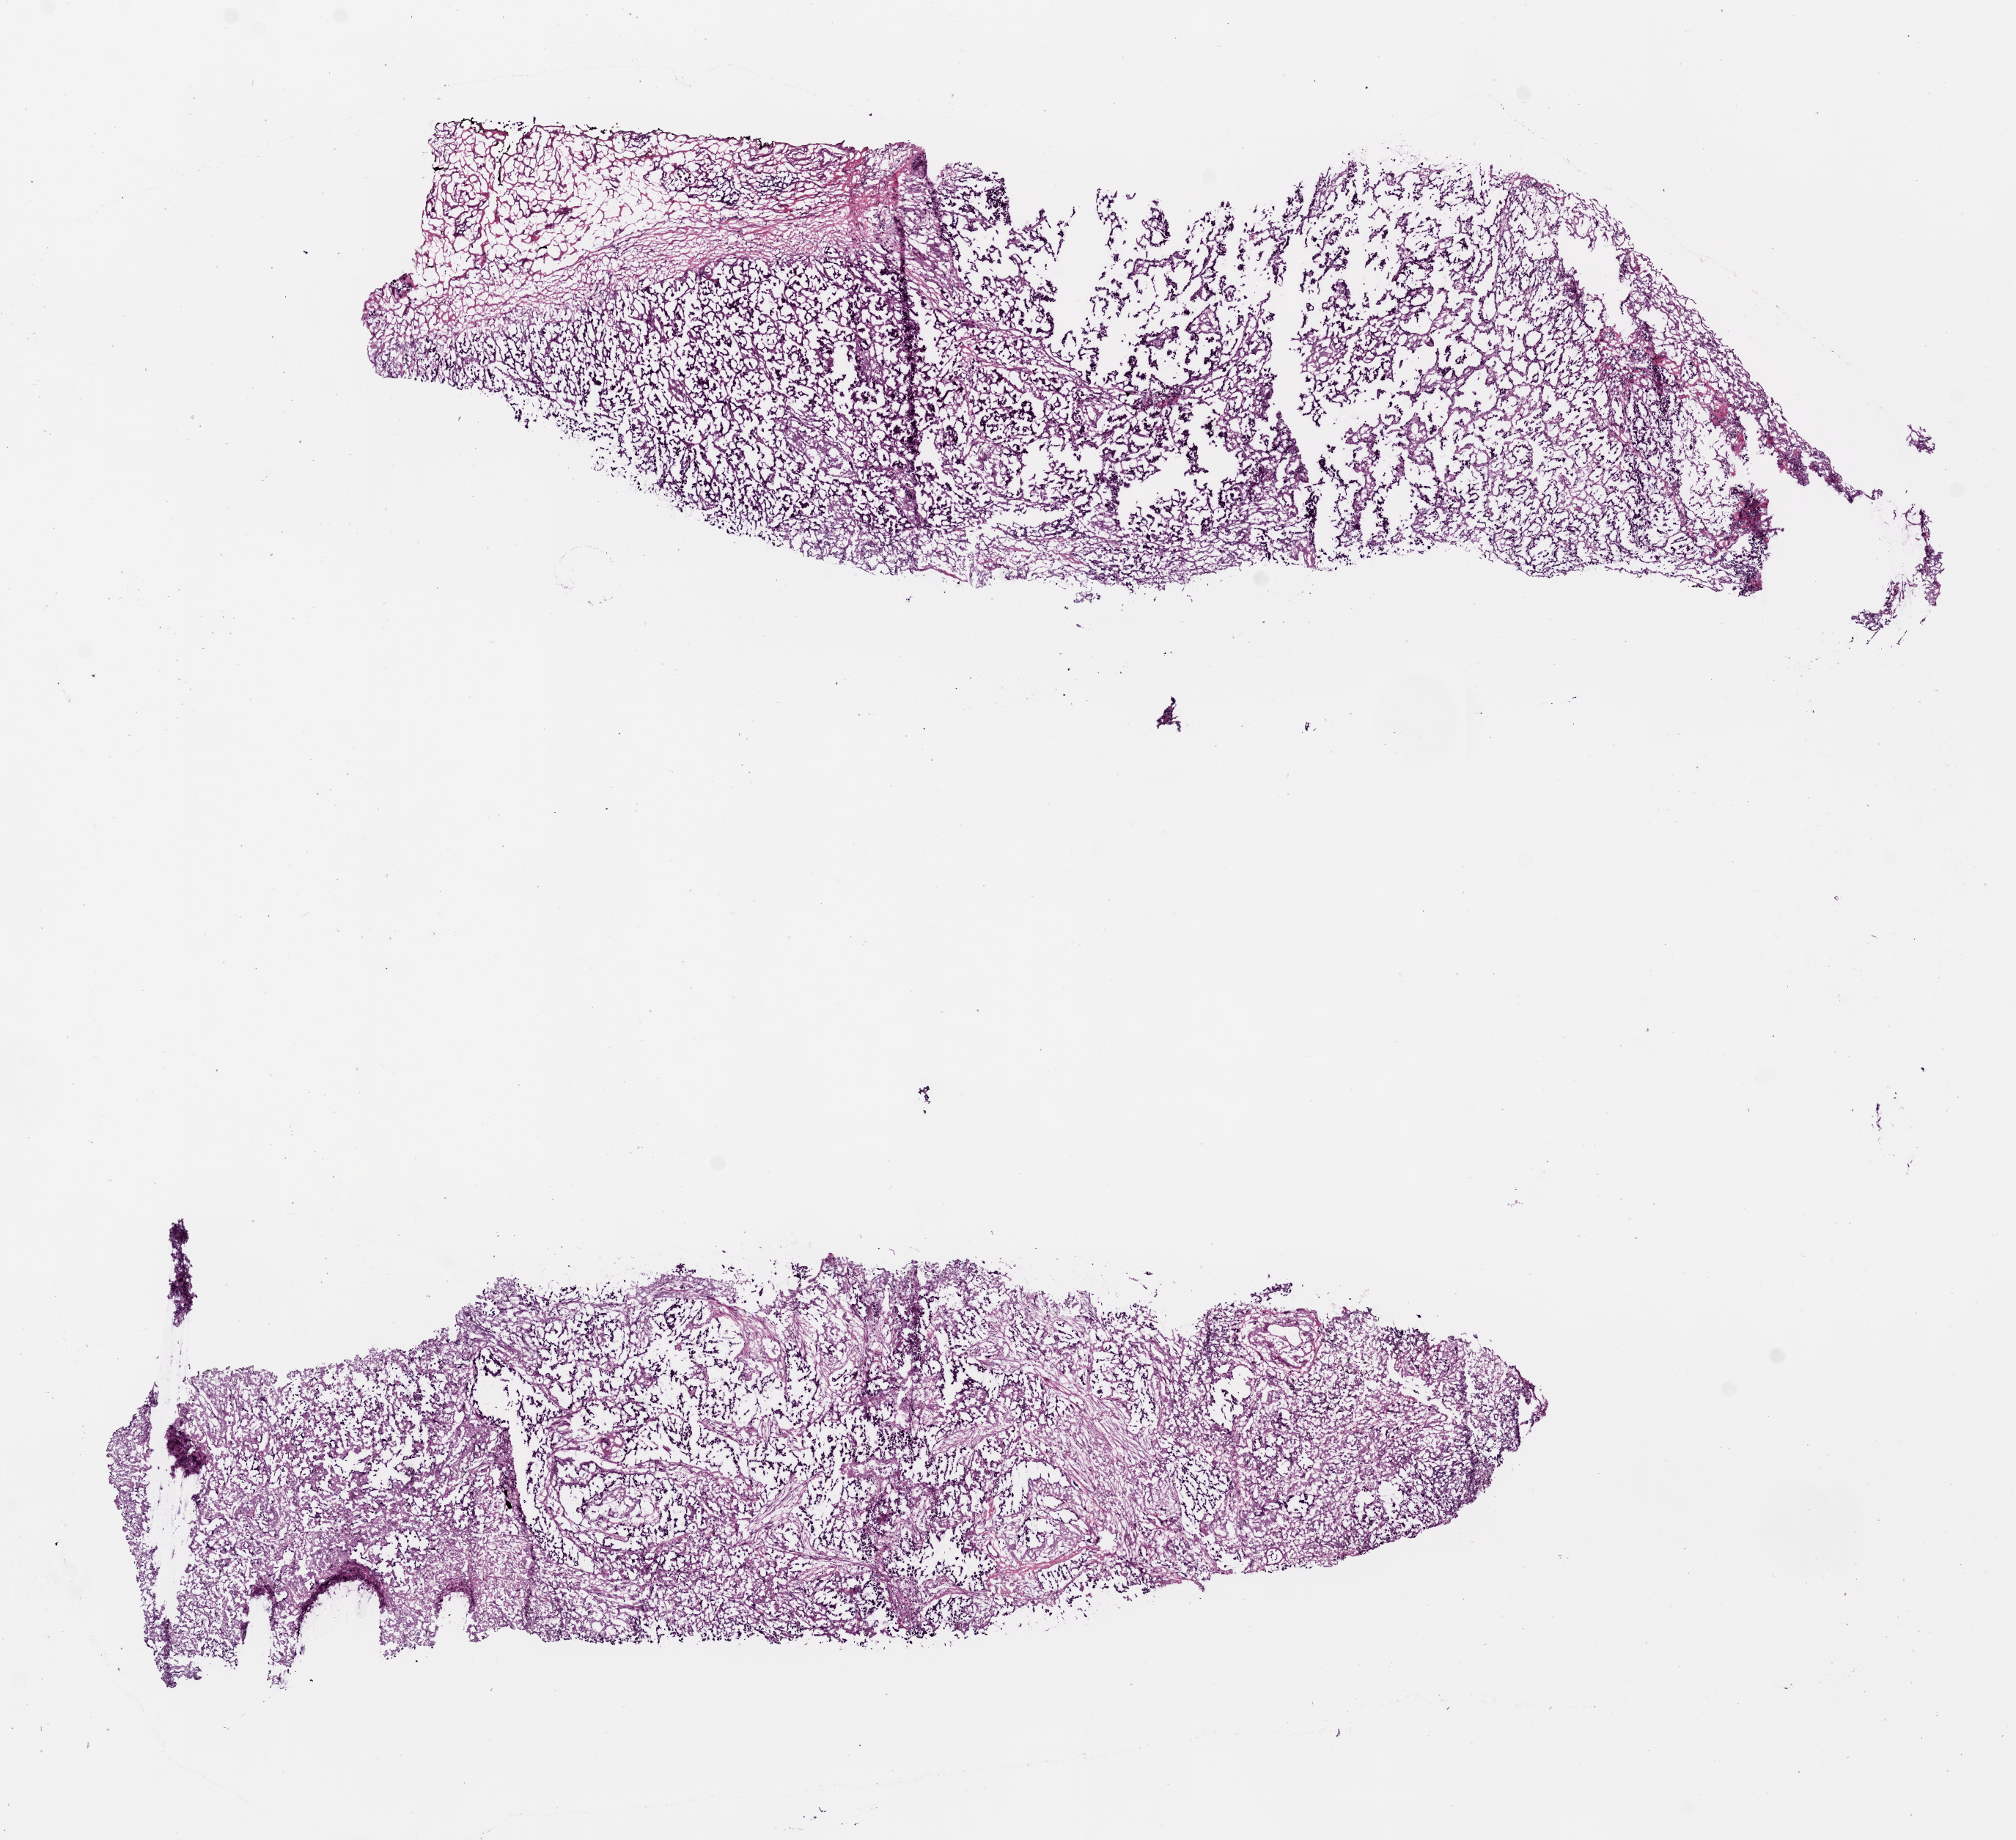
Whole-slide histology image, Hematoxylin and eosin (H&E) stained — whole scanned area (about 11.0 x 10.1 mm, acquisition: 20x scan) shown as a low-resolution overview; frozen section; sample: primary tumour, lung. Patient: female, age at initial diagnosis 69 years. Composition of this section per pathologist review: tumour cells 80%, tumour nuclei 75%, normal cells 5%, stromal cells 15%, necrosis 0%.
AJCC pathologic stage: IIIA. Diagnosis: Adenocarcinoma, NOS (middle lobe, lung).